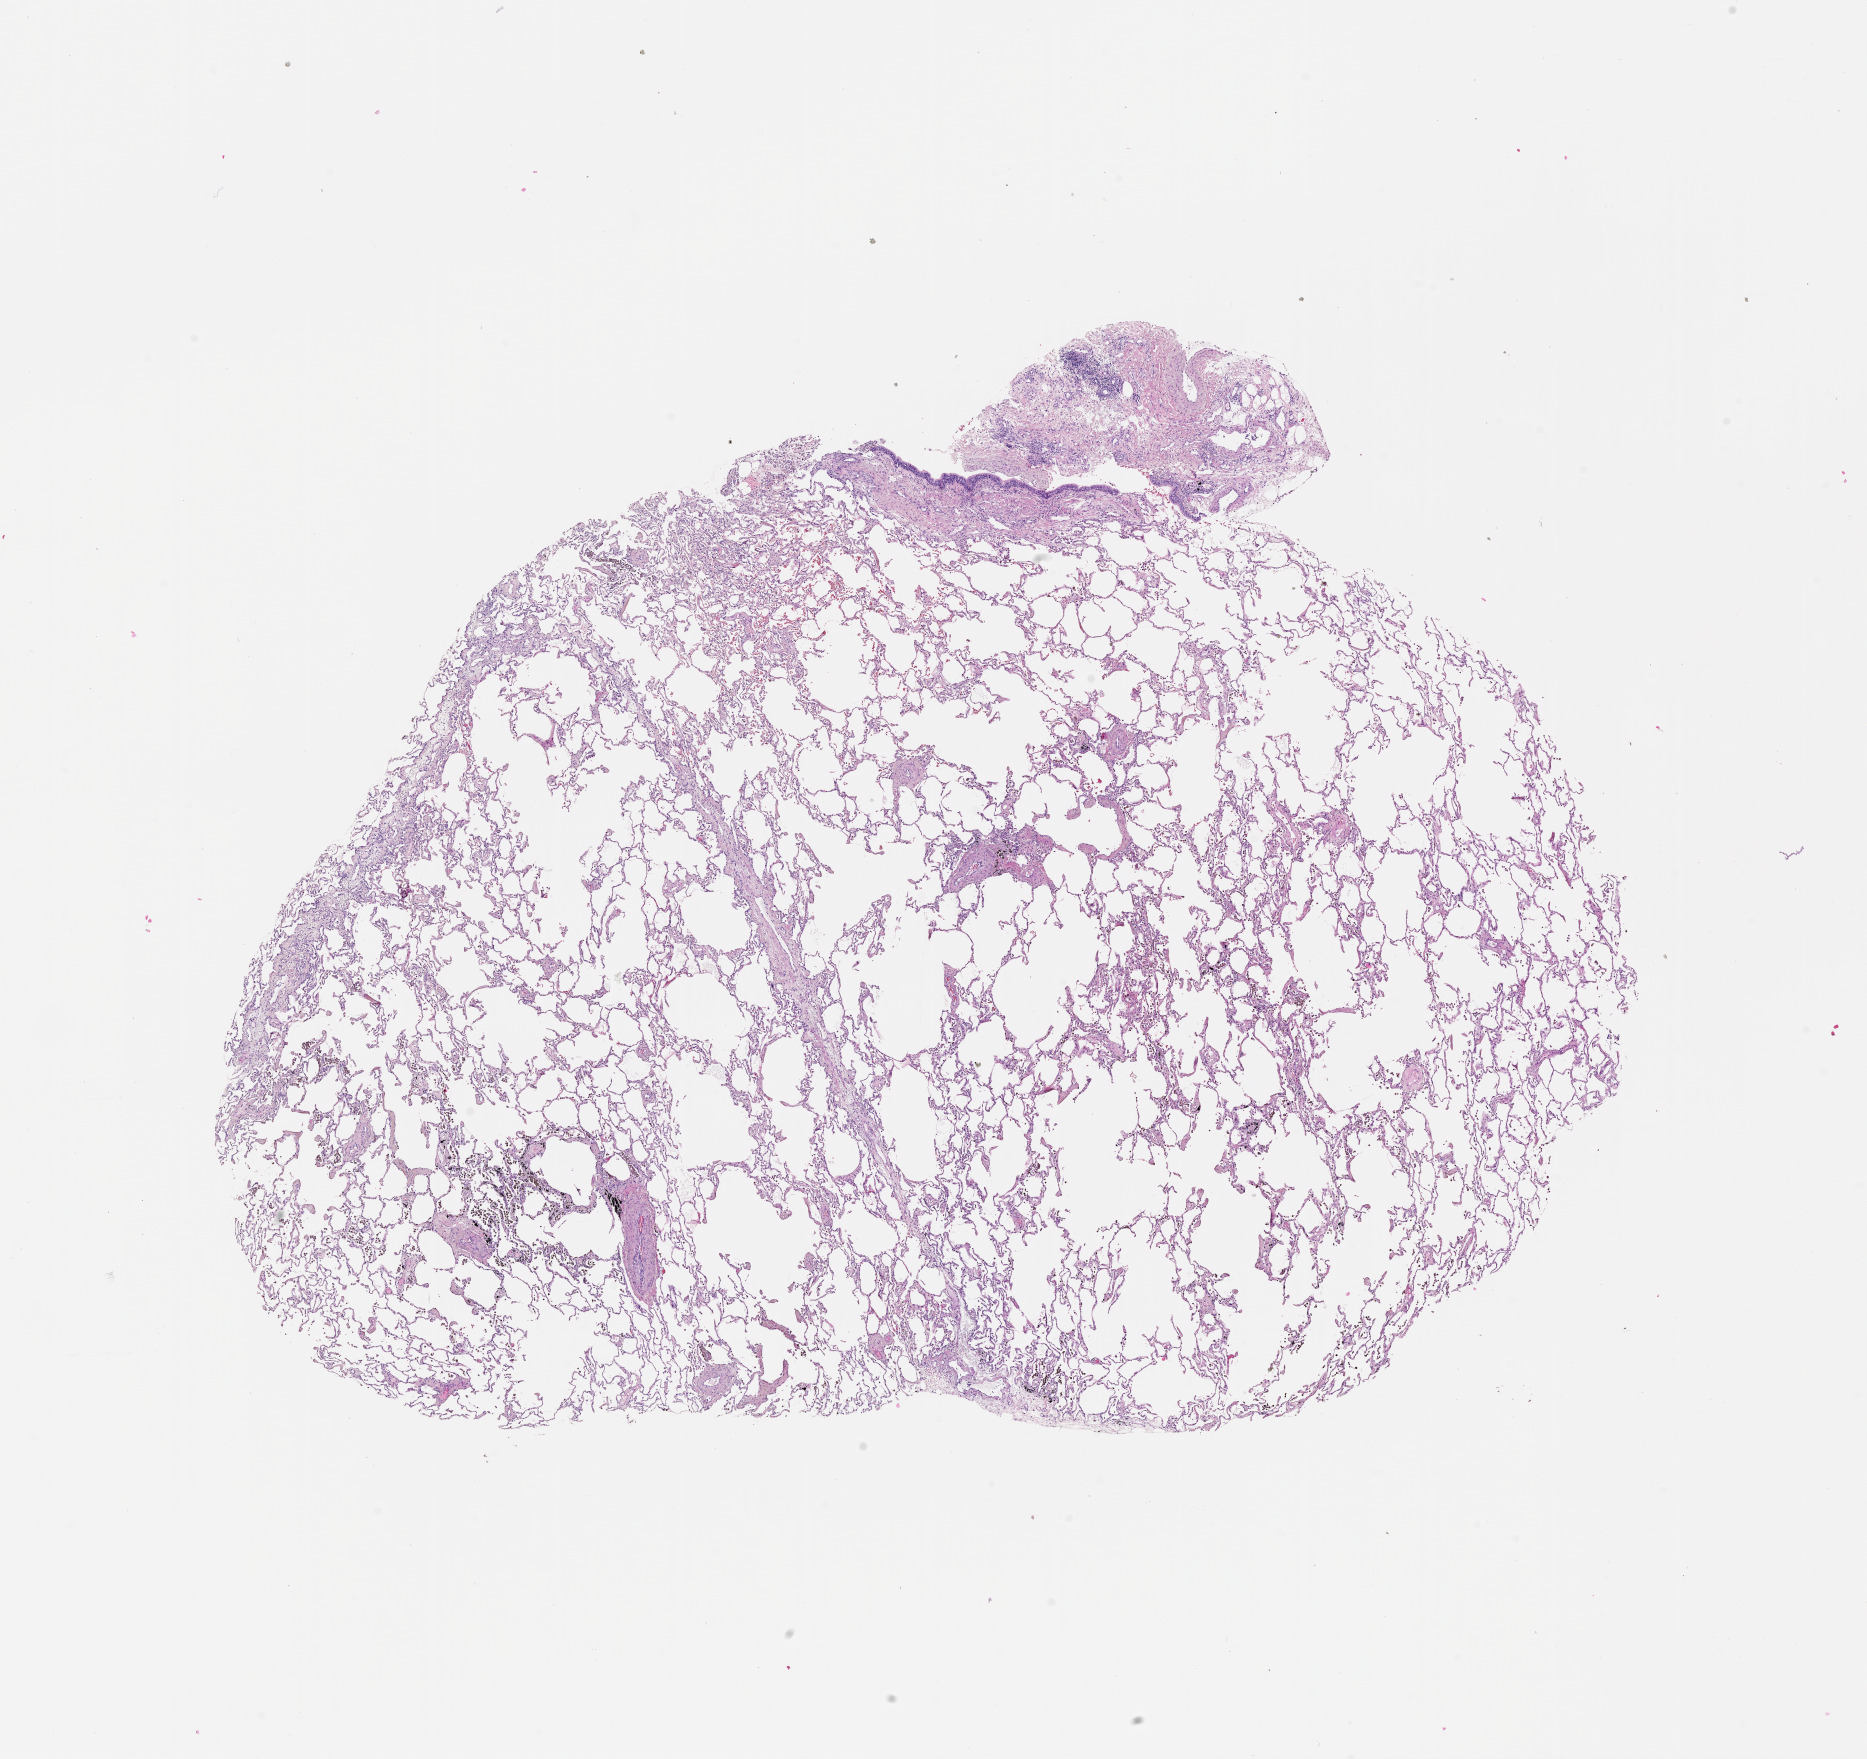
Whole-slide histology image, Hematoxylin and eosin (H&E) stained, shown as a low-resolution overview of the whole scanned area (about 15.0 x 14.2 mm, acquisition: 20x scan), normal (non-tumour) tissue sample, lung. 60-year-old male patient.
This section: normal (non-tumour) tissue from the same patient. Patient diagnosis (cohort enrolment): squamous cell carcinoma (lung).